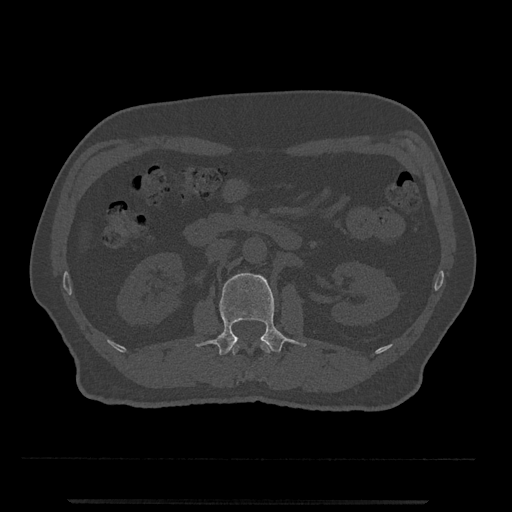
CT including the spine, one axial slice; position 282 of 797 along the scan axis; reconstruction kernel Br40s/3; 120 kVp; bone window (W 1800 / L 400 HU); 0.5 mm slice thickness; 512 × 512 image matrix, field of view 419 × 419 mm. Male patient, age 63 years. From the clinical record (not read from this slice): primary cancer: prostate.
Structures marked on this image (semi-automatic segmentation, software-assisted and operator-edited):
- L1 vertebra: bounding box (x1, y1, x2, y2) in pixels: (231, 341, 271, 355)
- L2 vertebra: (196, 273, 306, 356)